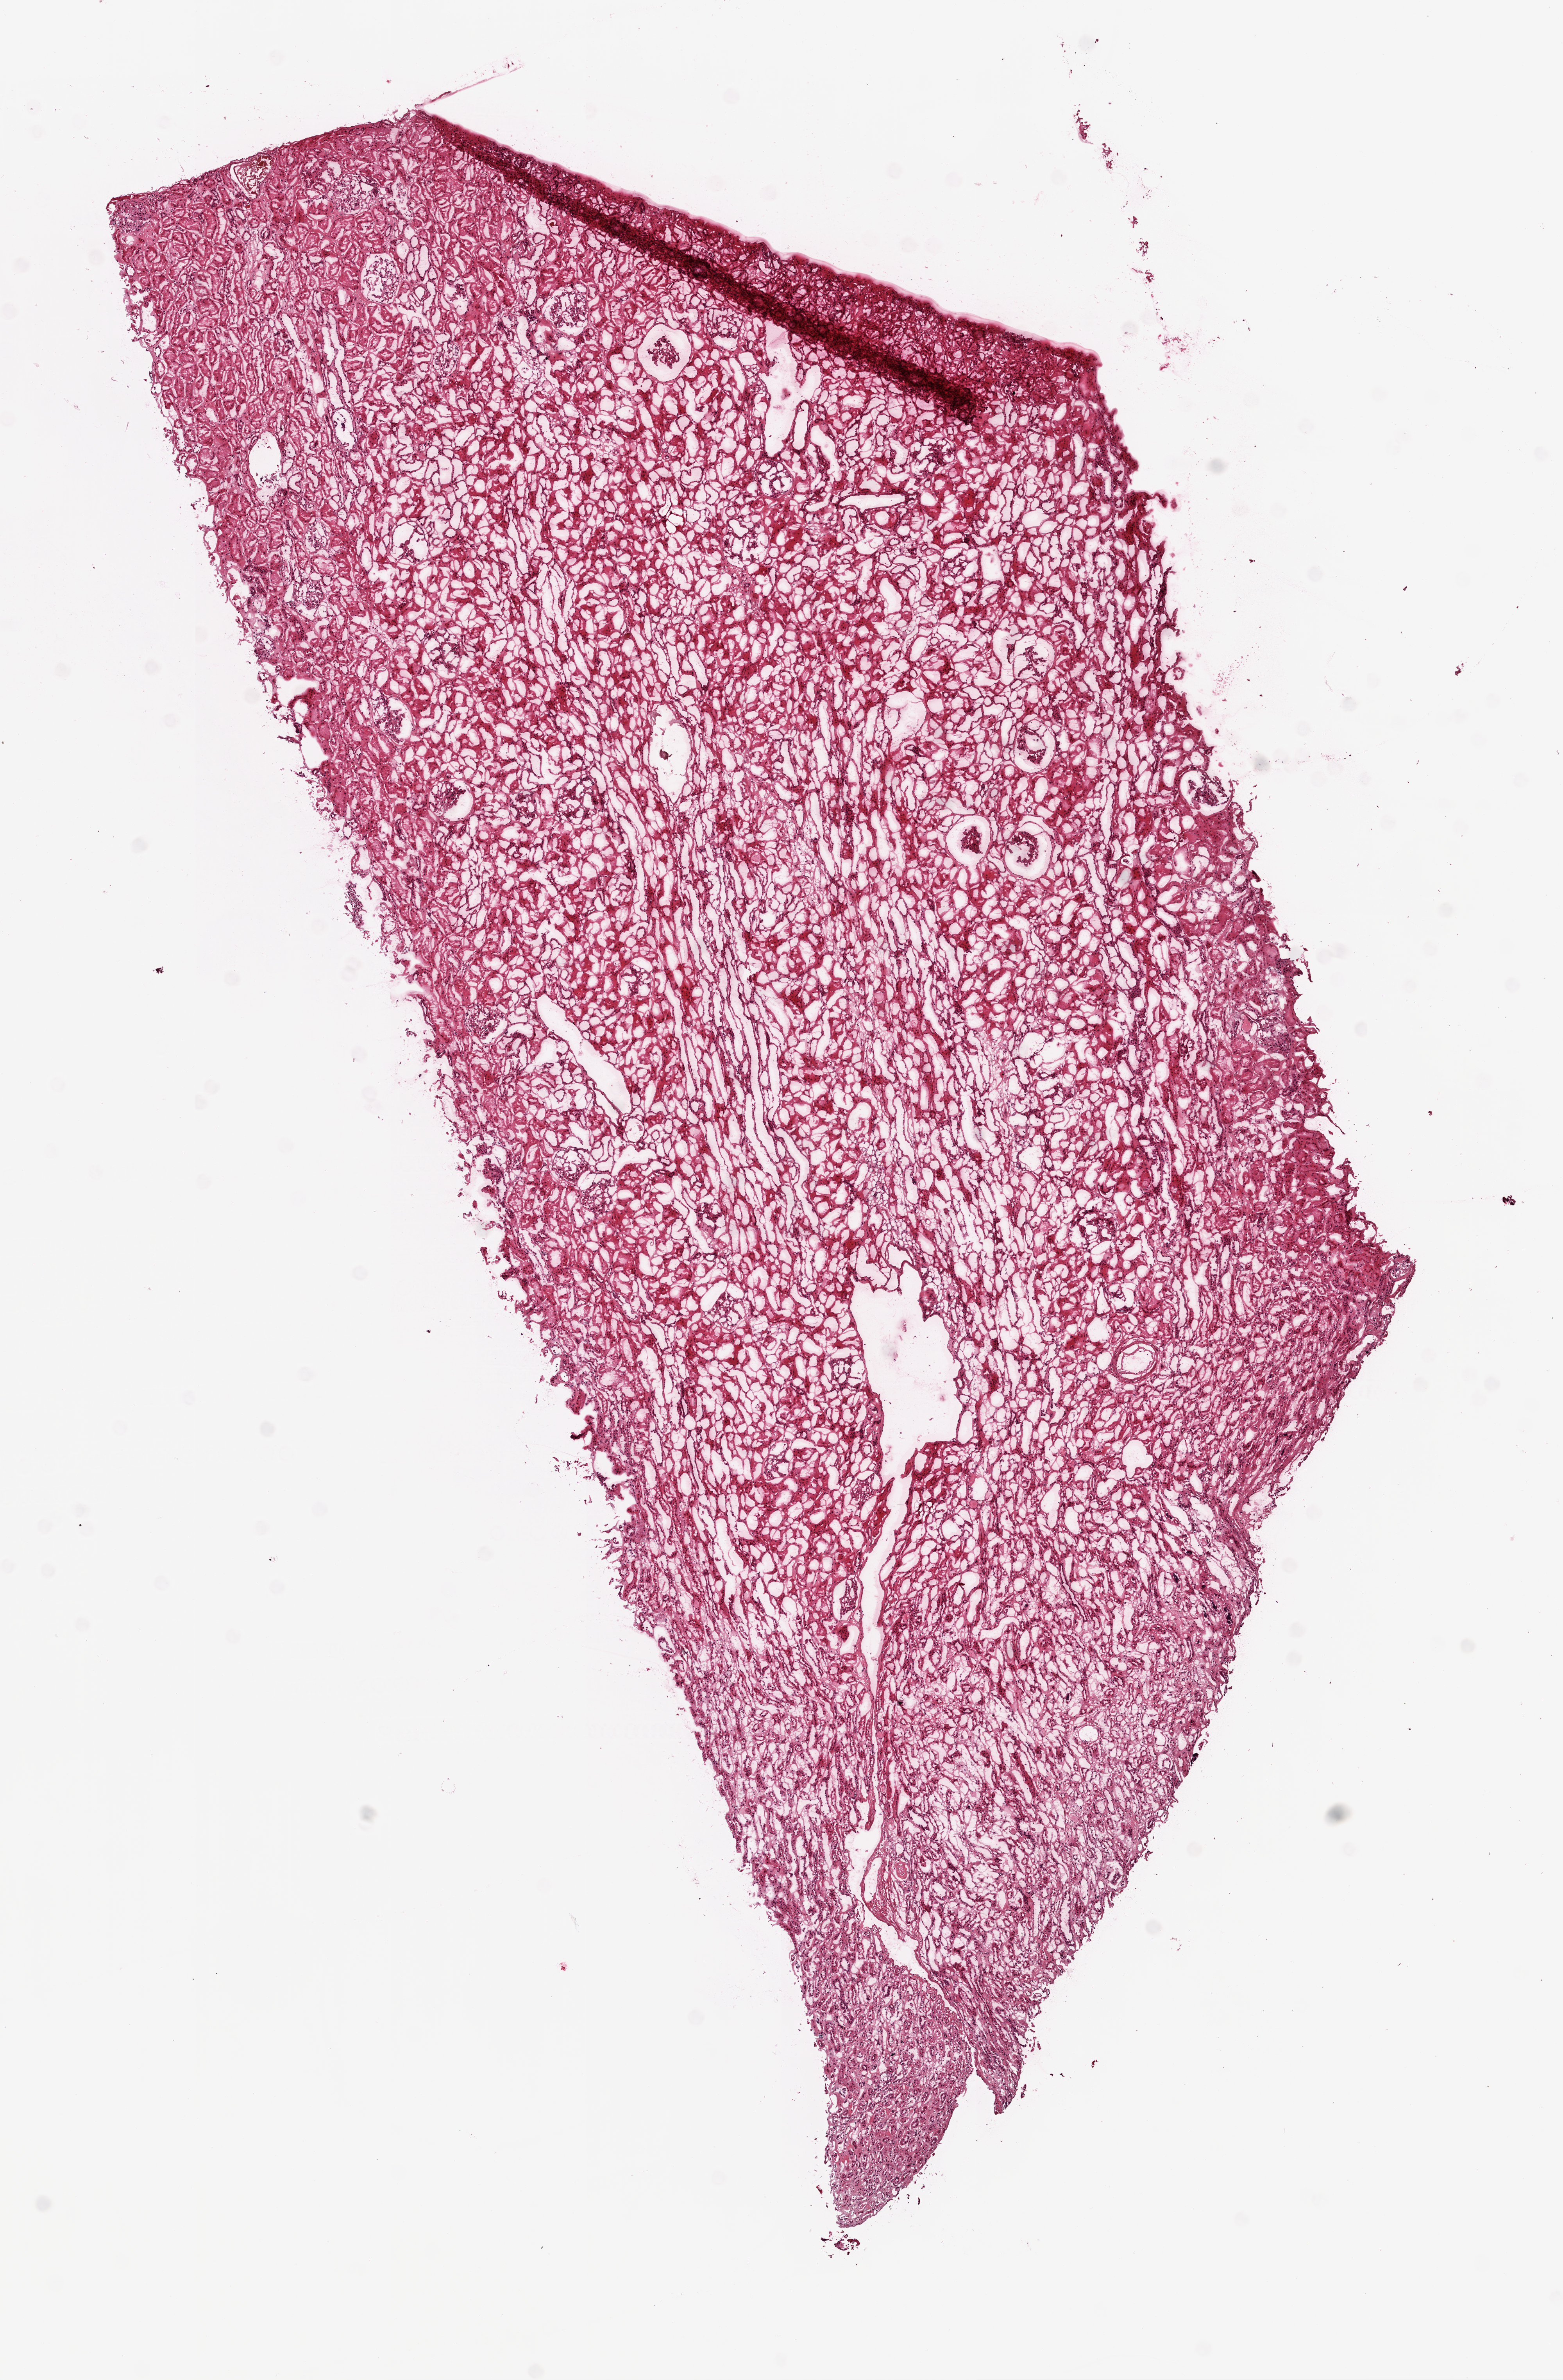
Digitized H&E-stained tissue section (whole slide), a low-resolution overview of the entire scanned area, about 8.0 x 12.2 mm (acquisition: 20x scan); frozen section; kidney, solid tissue normal (non-tumour tissue) sample. Male, age 52 years at initial diagnosis.
This section: solid tissue normal sample (biorepository sample class). Patient diagnosis: Clear cell adenocarcinoma, NOS.